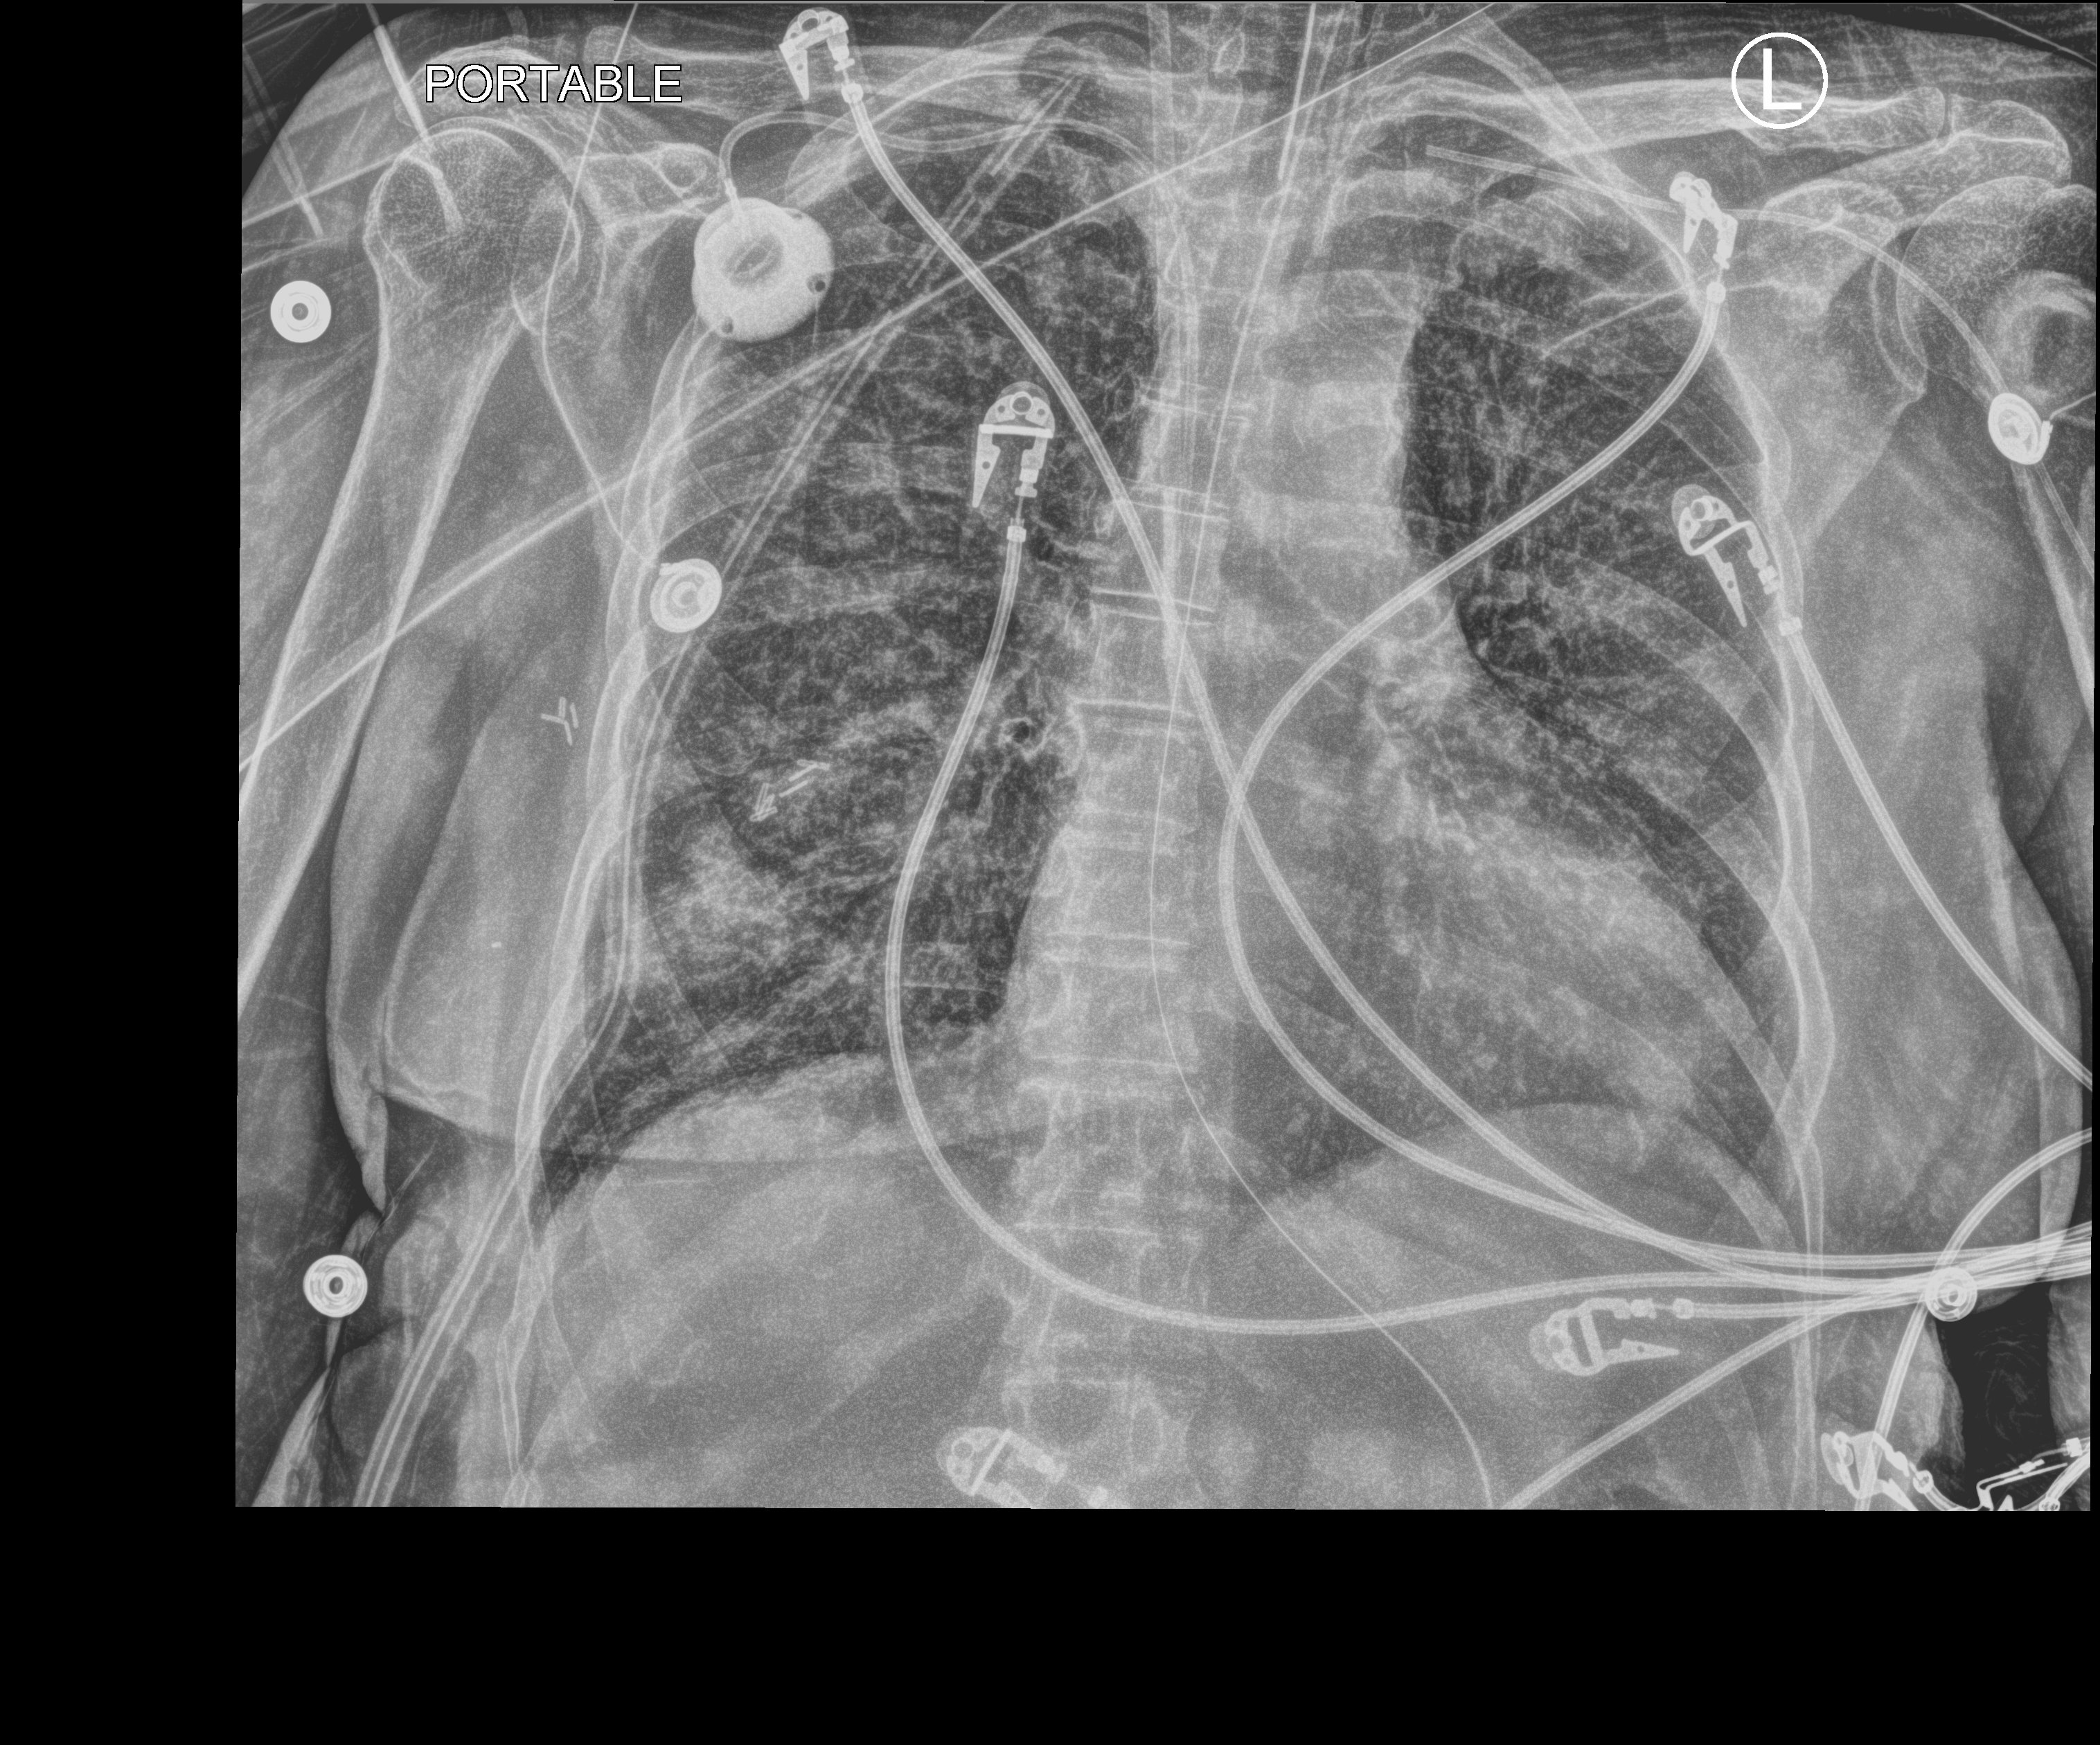
Bedside chest radiograph (computed radiography), anteroposterior (AP) projection. Female patient hospitalised with COVID-19, age 60–74 years.
Admission-level facts for this patient (not findings on this image; timing relative to this image not recorded):
- other chronic lung disease (admission record): no
- mechanically ventilated during this hospital stay: yes